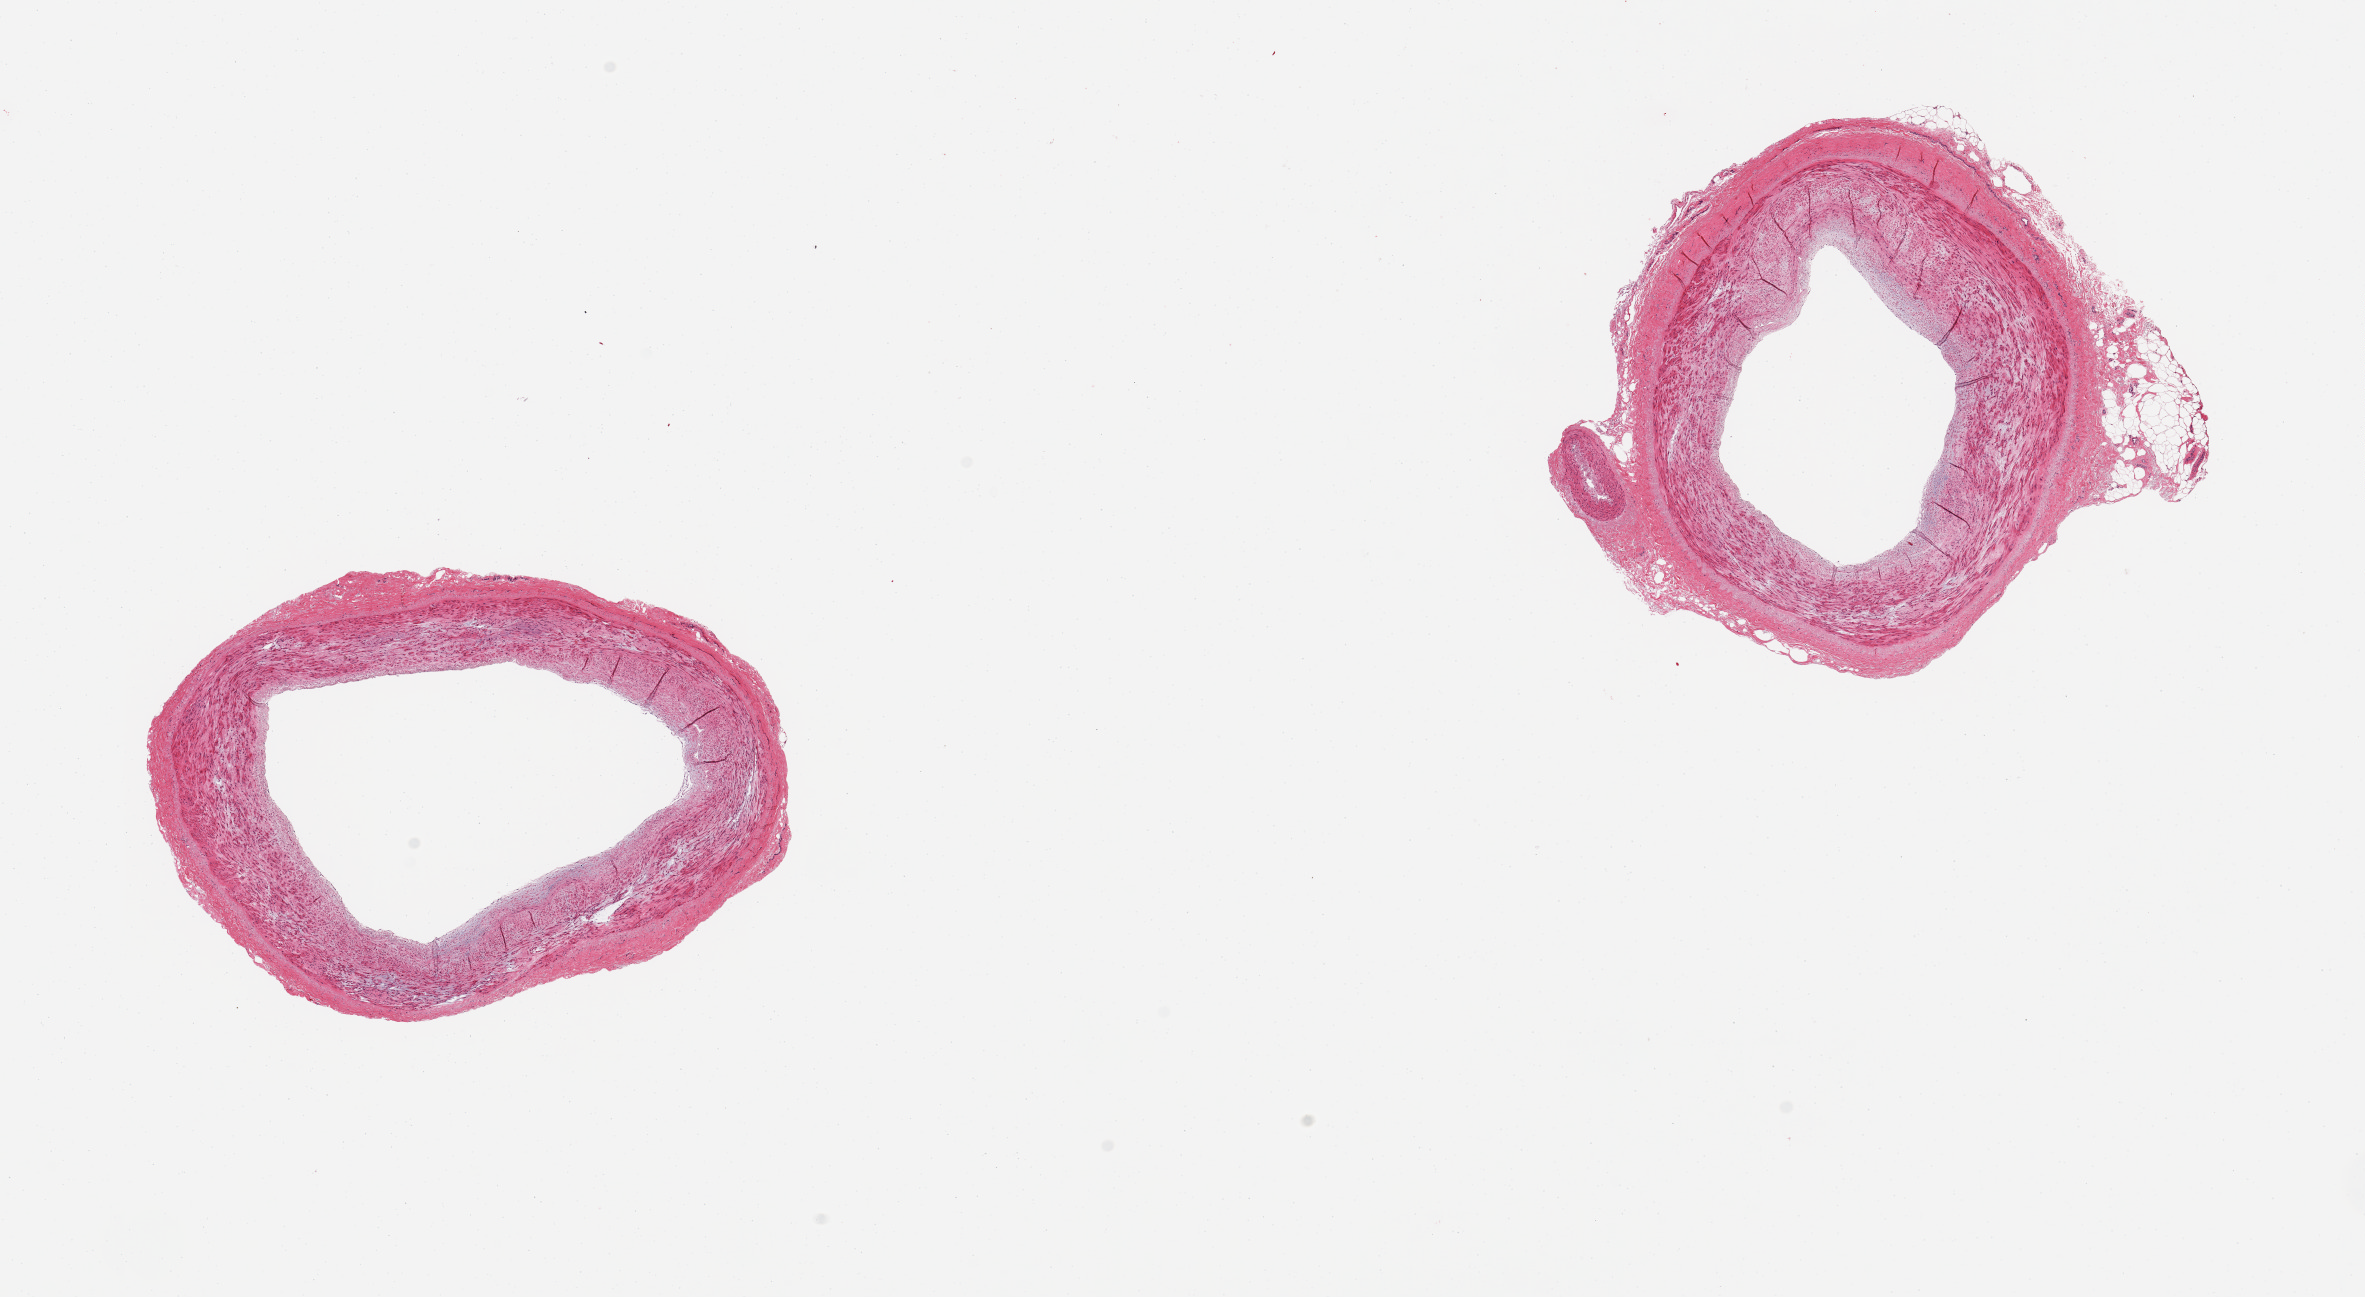
H&E whole-slide image, brightfield, a low-resolution overview of the entire scanned area, about 18.7 x 10.3 mm. PAXgene-fixed paraffin-embedded (PFPE) section. Section of tibial artery (target tissue). Donor tissue sample. Donor sex: female.
Reviewer comment on this tissue sample: 2 pieces, good clean sections, no adherent fat, no atherosis.